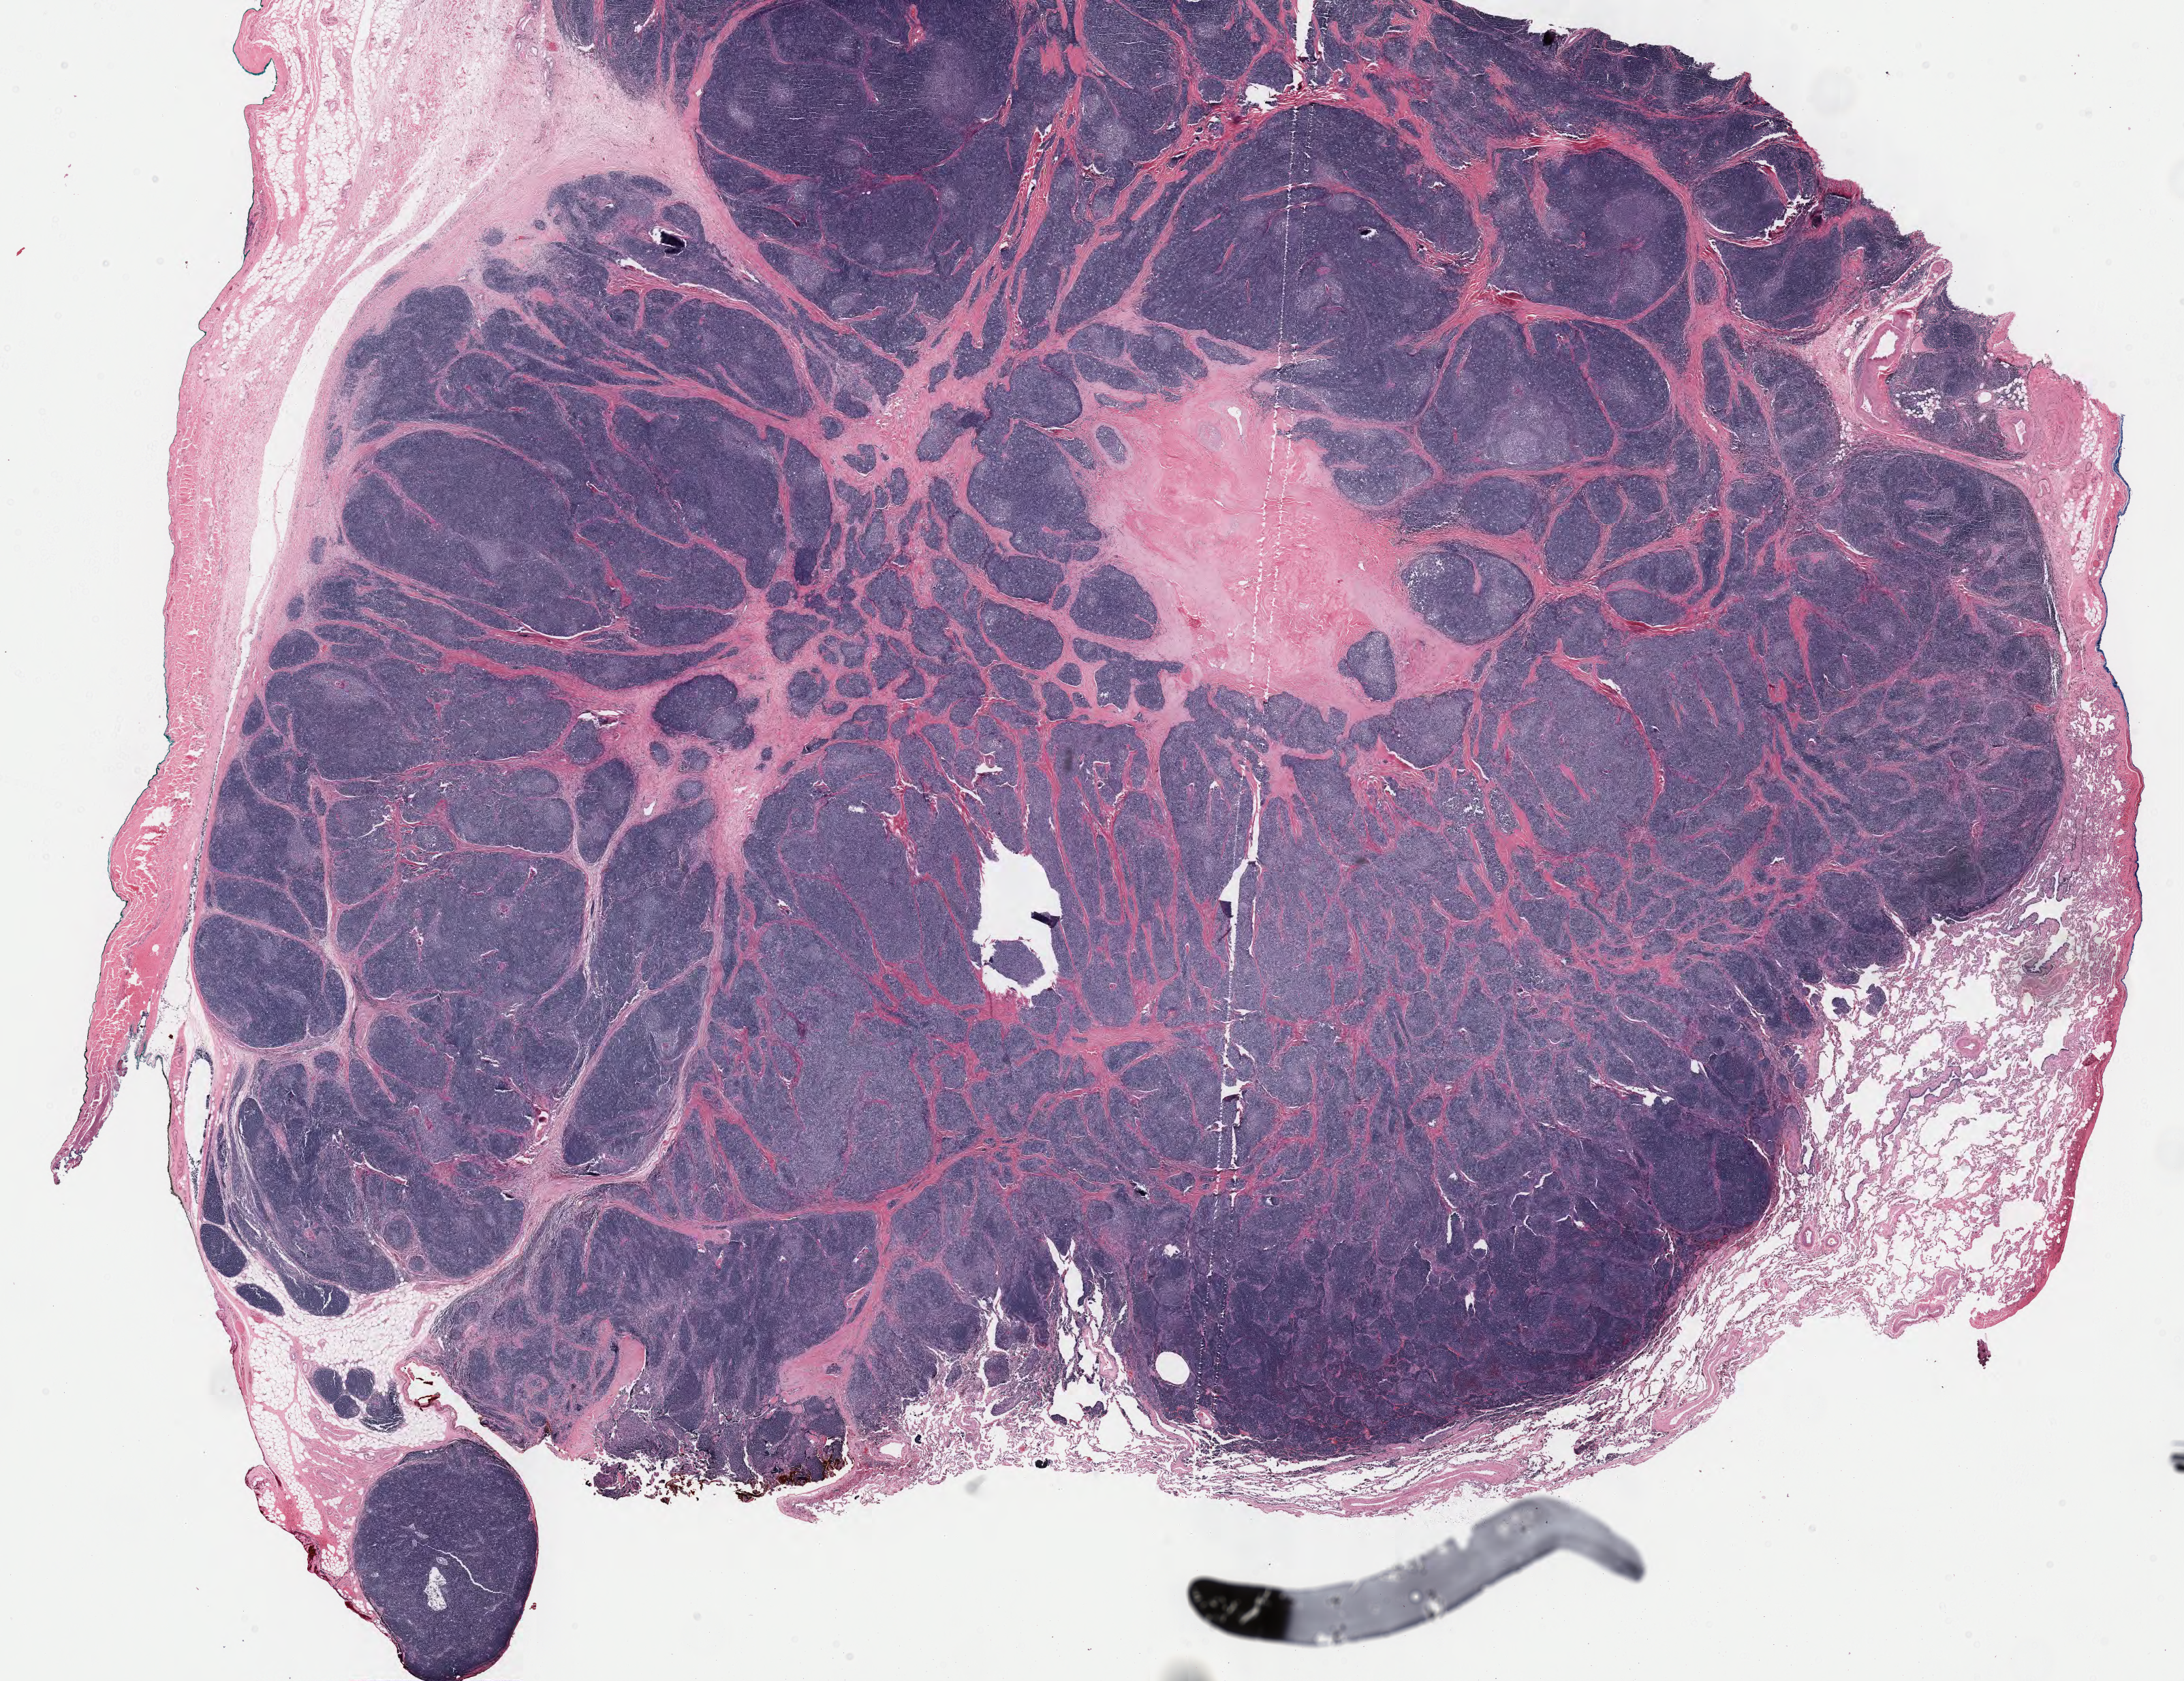
Digitized Hematoxylin and eosin (H&E) stained tissue section (whole slide), low-resolution overview of the scanned area, about 25.4 x 19.6 mm (acquisition: 40x scan). Formalin-fixed paraffin-embedded (FFPE) diagnostic section. Primary tumour sample from the thymus. Female, age 57 years at initial diagnosis.
Pathologic diagnosis: Thymoma, type B1, NOS.